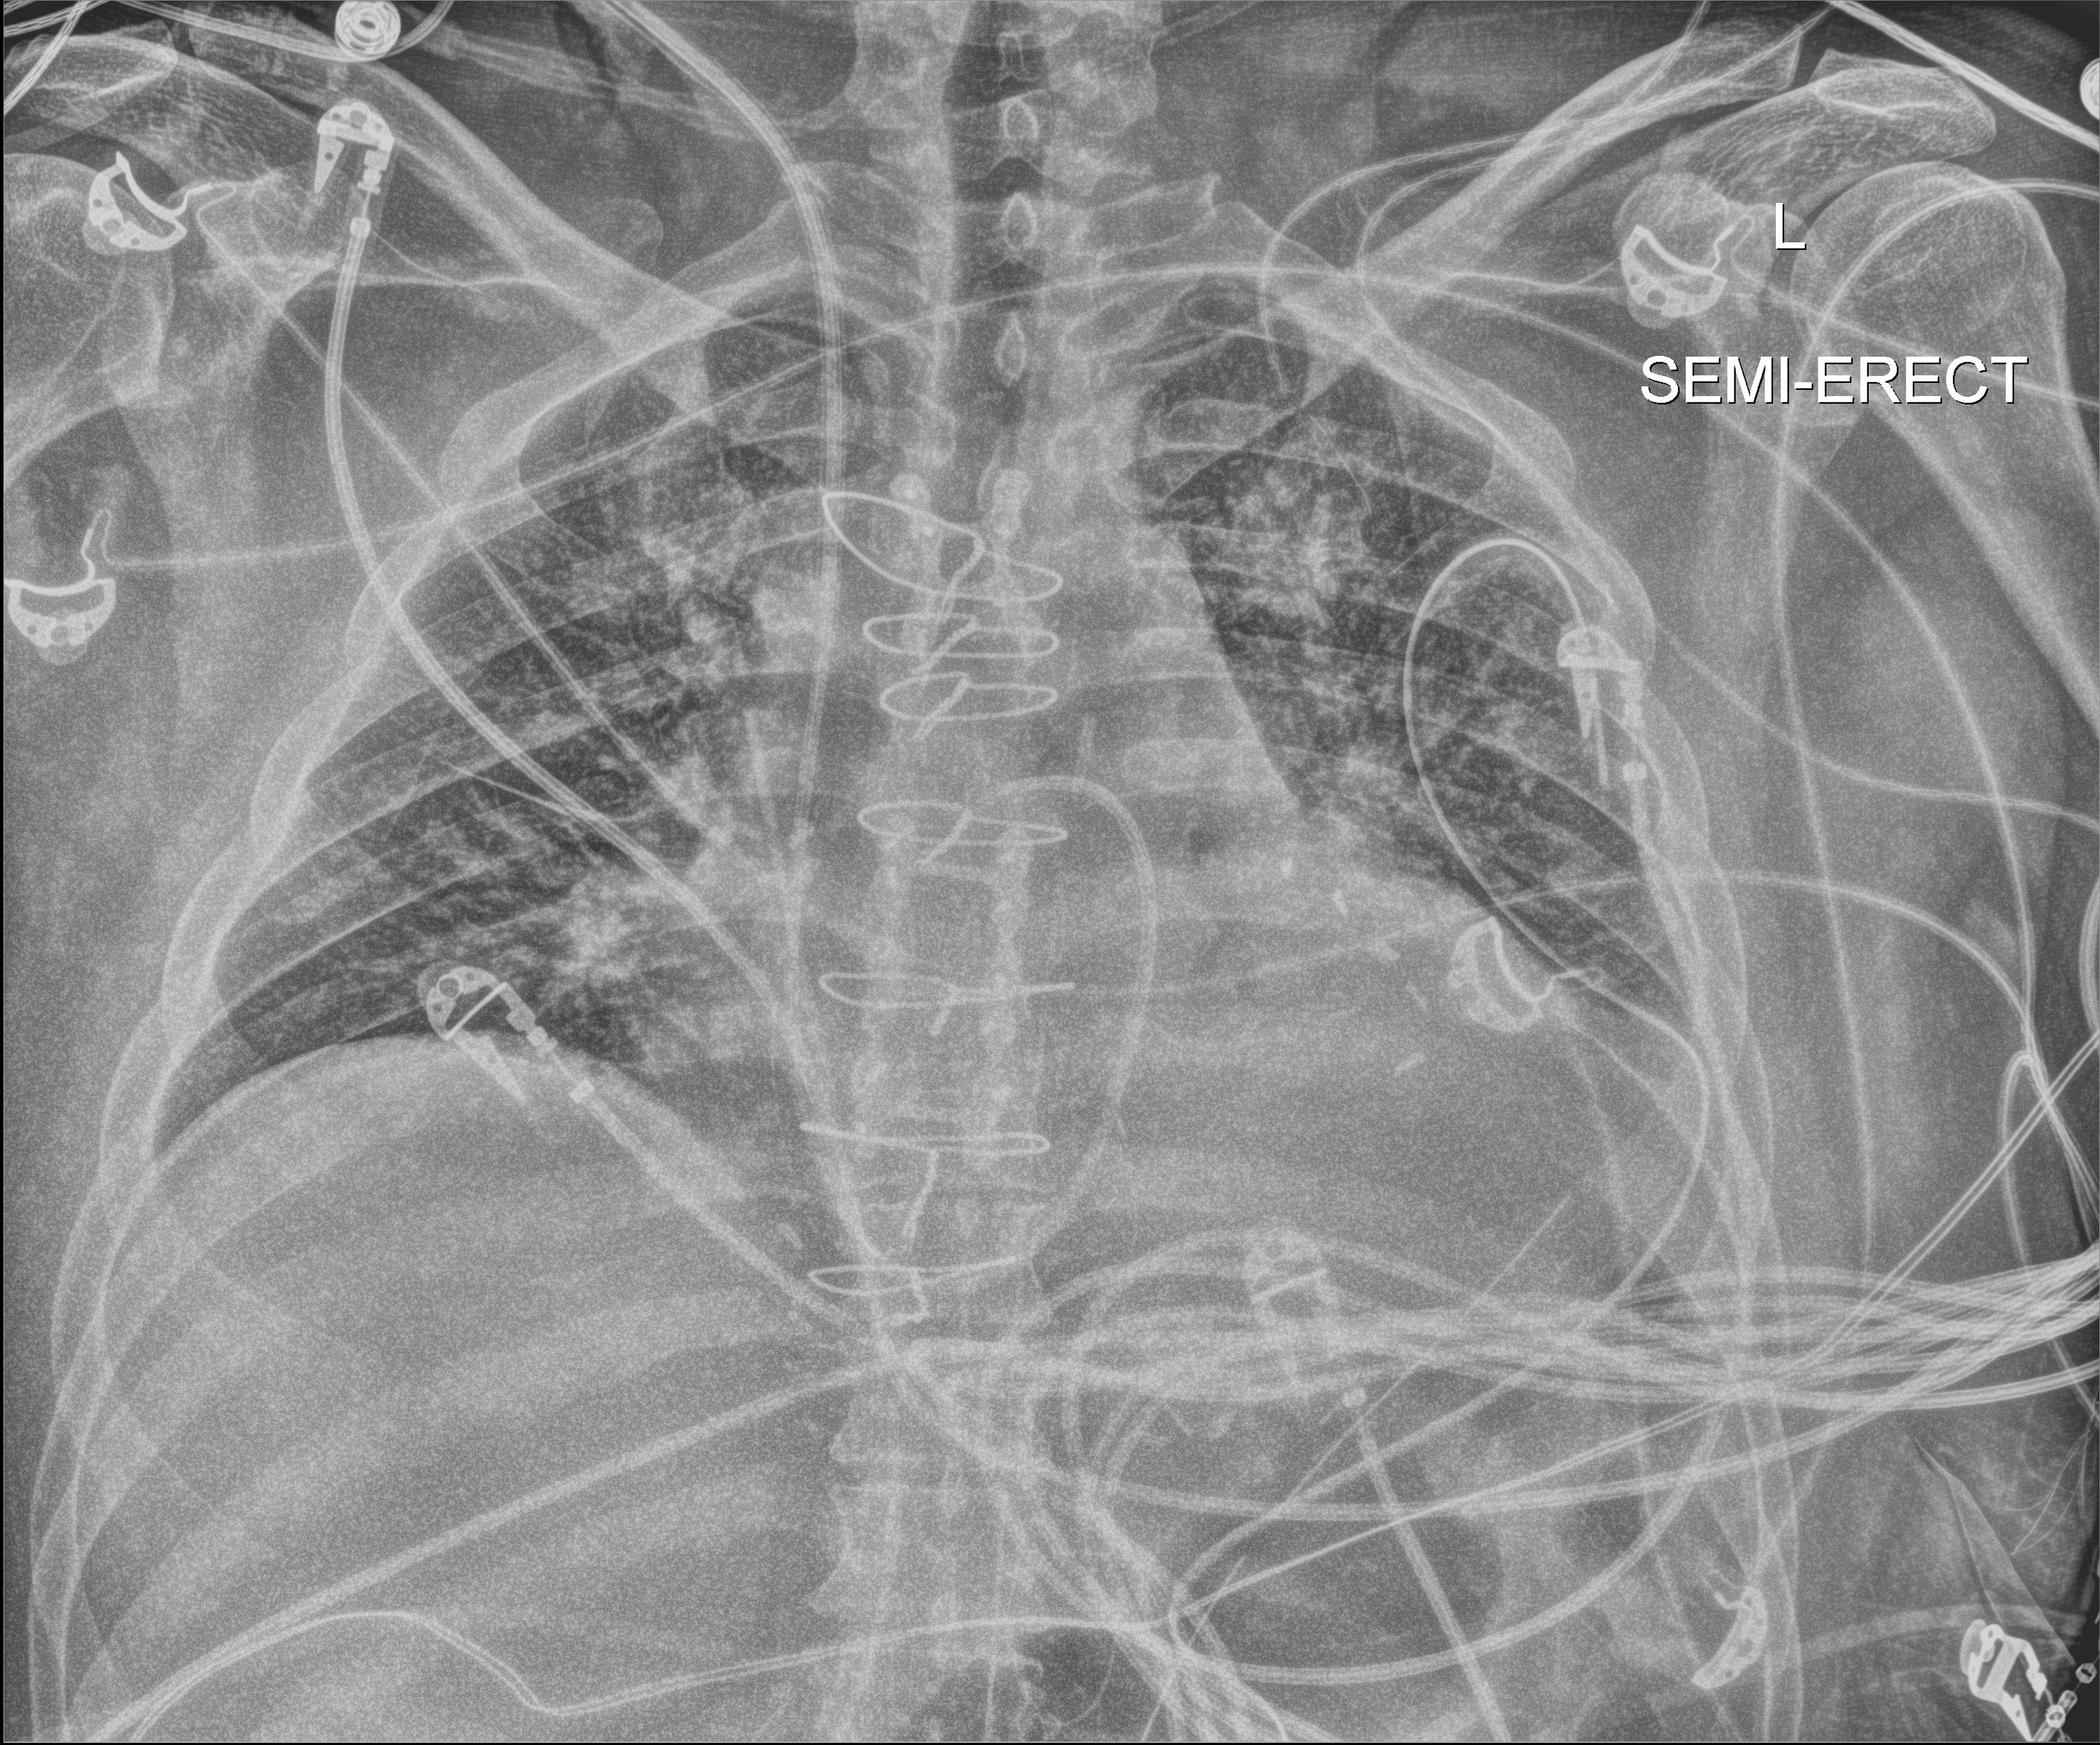
Portable chest radiograph, anteroposterior (AP) projection. Male patient hospitalised with COVID-19, age 18–59 years.
From the hospital-stay record, not from the radiograph (when in the stay this image was taken is not recorded):
- mechanically ventilated during this hospital stay: no
- admitted to intensive care during this hospital stay: no